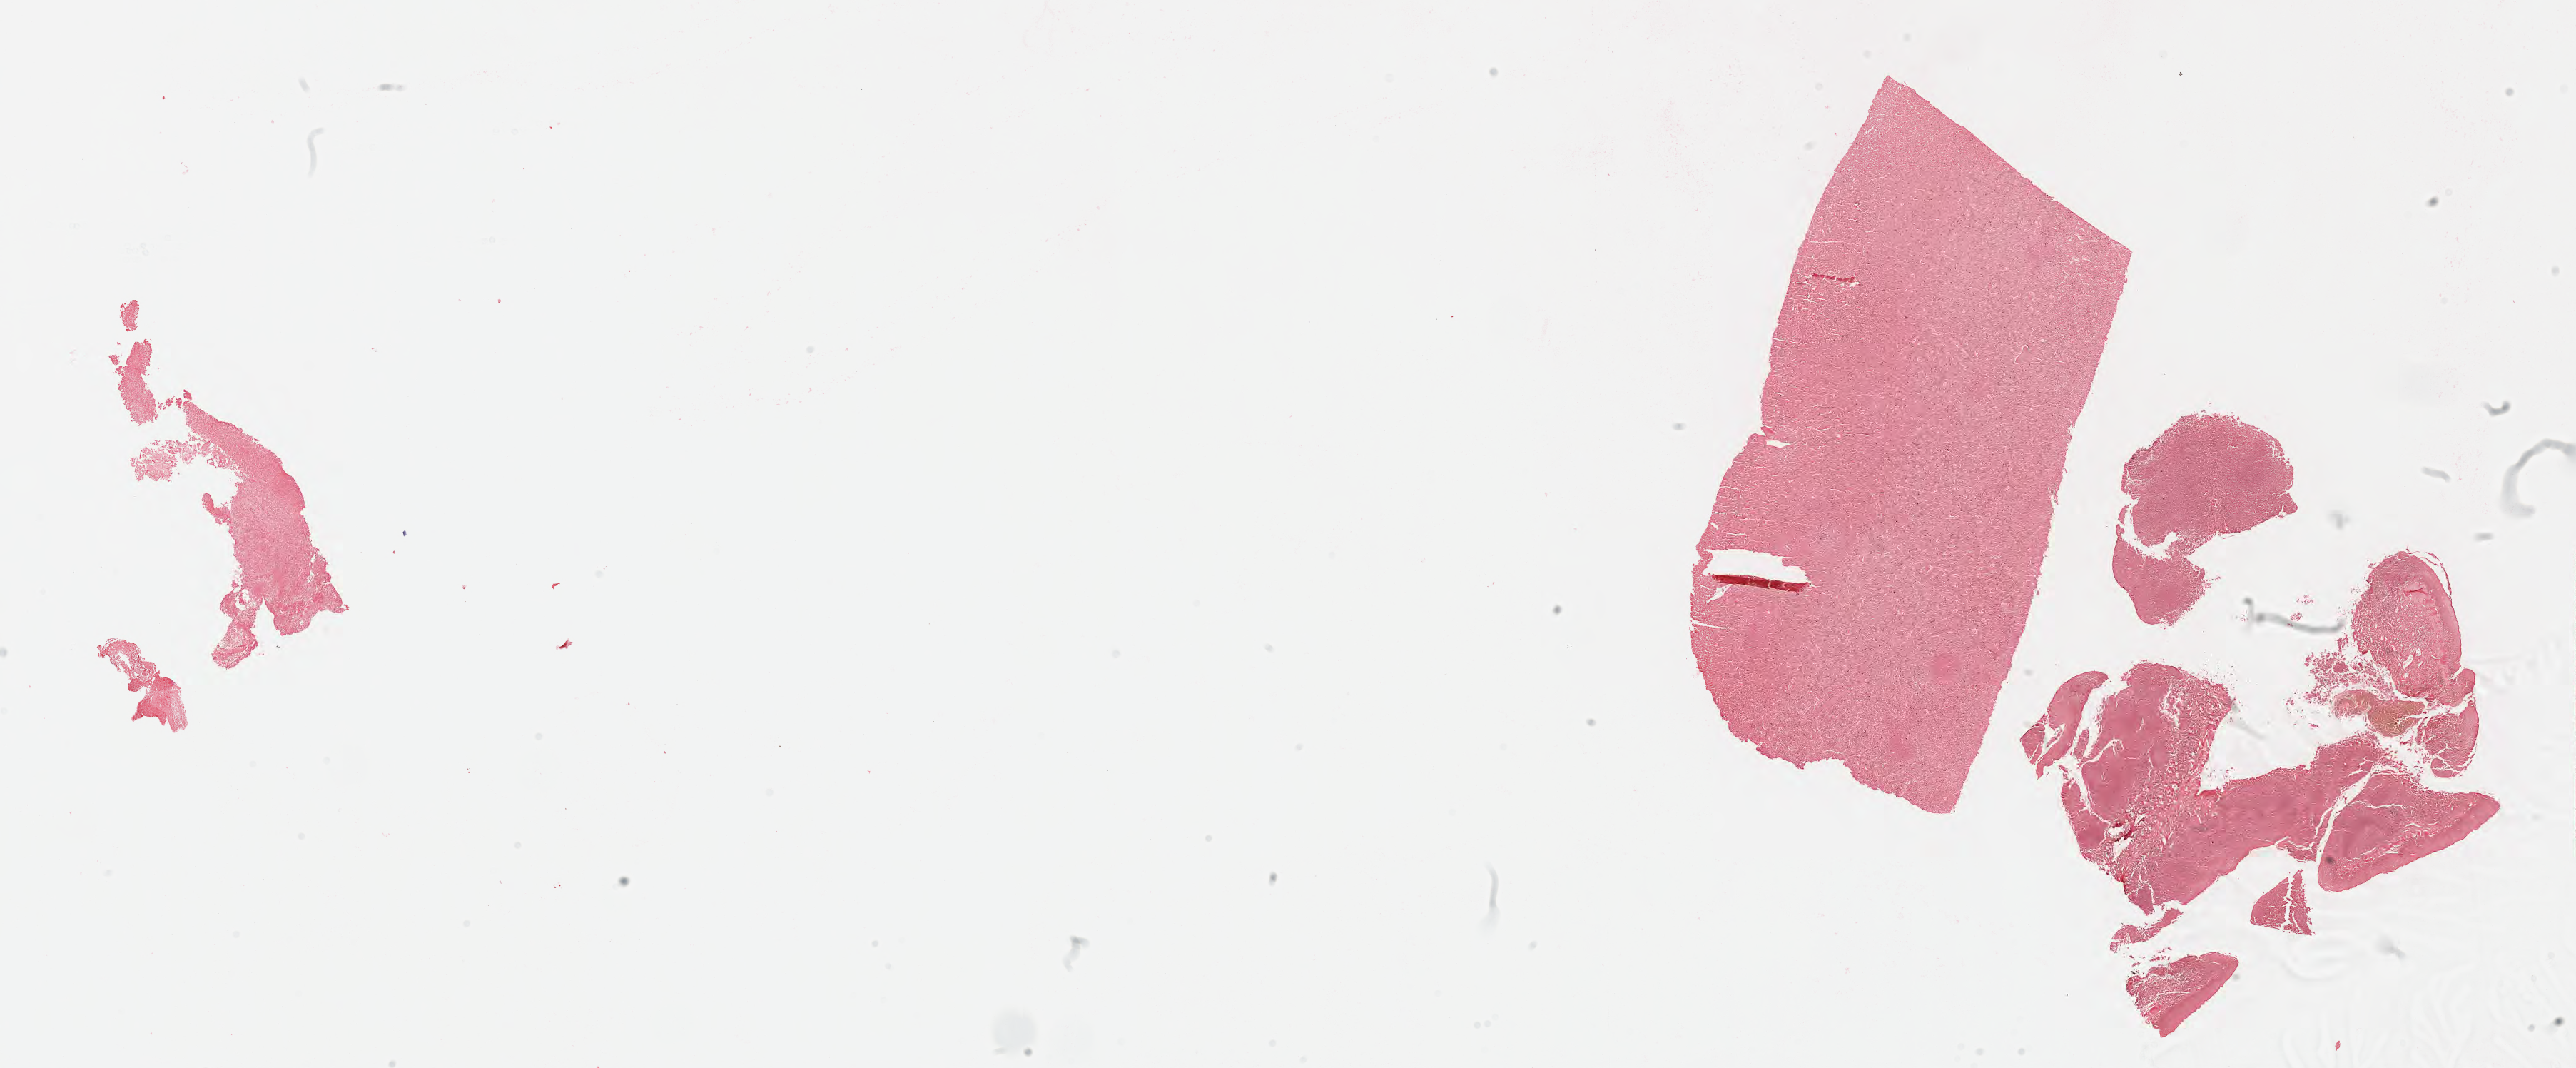
In-situ hybridisation whole-slide image, Epstein–Barr virus-encoded RNA (EBER) probe, a low-resolution overview of the entire scanned area, about 29.2 x 12.1 mm, tumor tissue. Patient: female, aged 27.
• diagnosis: Diffuse large B-cell lymphoma, NOS